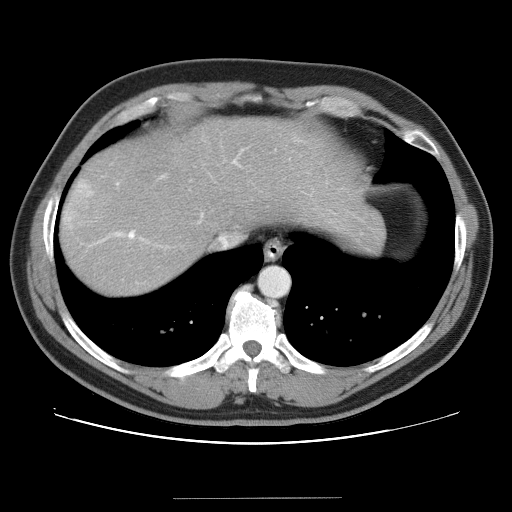
Contrast-enhanced abdominal CT (liver protocol), one axial slice; slice 32 of 40 in the series (ordered by position); soft-tissue window (W 400 / L 40 HU); 512 × 512 image matrix, field of view 380 × 380 mm. Case-level facts recorded for this patient, not image findings: diagnosis: hepatocellular carcinoma (patient treated with transarterial chemoembolisation; whether this scan precedes or follows treatment is not stated here); TNM stage (as recorded): Stage-IVA; Child-Pugh class: B.
Structures marked on this image (semi-automatically segmented with operator editing):
- abdominal aorta: bounding box (x1, y1, x2, y2) in pixels: (260, 267, 289, 296)
- liver parenchyma outside the tumour (the mass and vessels are separate outlines, so this box may not span the whole liver): (60, 118, 386, 294)
- mass: (63, 177, 110, 232)
- liver vessels: (98, 160, 237, 243)